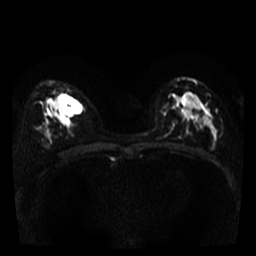
Breast MRI, one axial slice; diffusion-weighted series; image 2 of 4 stored at this slice position (different b-values; order by instance number); 3 T; 256 × 256 image matrix, field of view 280 × 280 mm. Female patient.
Outlined on this slice (outlined manually by an expert reader):
- tumour on diffusion-weighted imaging: box from (x=60, y=97) to (x=78, y=116) px